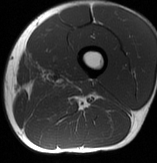
MRI of an extremity soft-tissue mass, one axial slice; slice 17 of 70 in the series (ordered by position); MR volume resampled by the dataset authors to the PET/CT grid (not the native acquisition matrix); 3.27 mm slice thickness; 157 × 163 image matrix, field of view 153 × 159 mm. Male patient. From the clinical record (not read from this slice): histological type: extraskeletal osteosarcoma; grade: high; site of the primary tumour: left adductur.
Outlined on this slice (expert contour drawn on MRI and transferred to this co-registered scan by the dataset authors):
- gross tumour volume (mass): bounding box <72,81,91,93> (left, top, right, bottom; pixels)